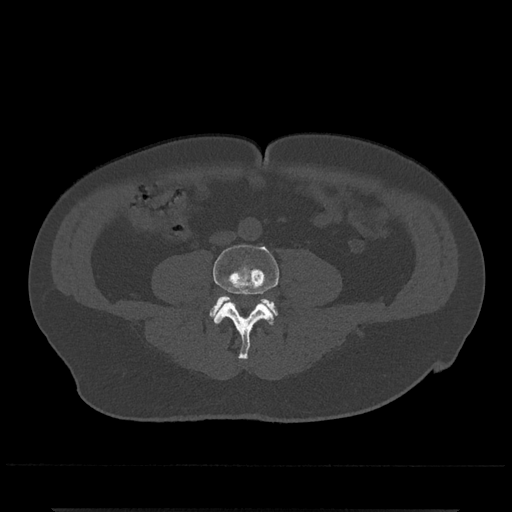
CT including the spine, one axial slice. Position 140 of 797 along the scan axis. Reconstruction kernel Br40s/3. 120 kVp. Bone window (W 1800 / L 400 HU). 512 × 512 image matrix, field of view 393 × 393 mm. Patient: male, 67 years. From the clinical record (not read from this slice): primary cancer: prostate.
Outlined on this slice (semi-automatically segmented with operator editing):
- L4 vertebra: bounding box <213,244,279,360> (left, top, right, bottom; pixels)
- L5 vertebra: <209,295,278,319>